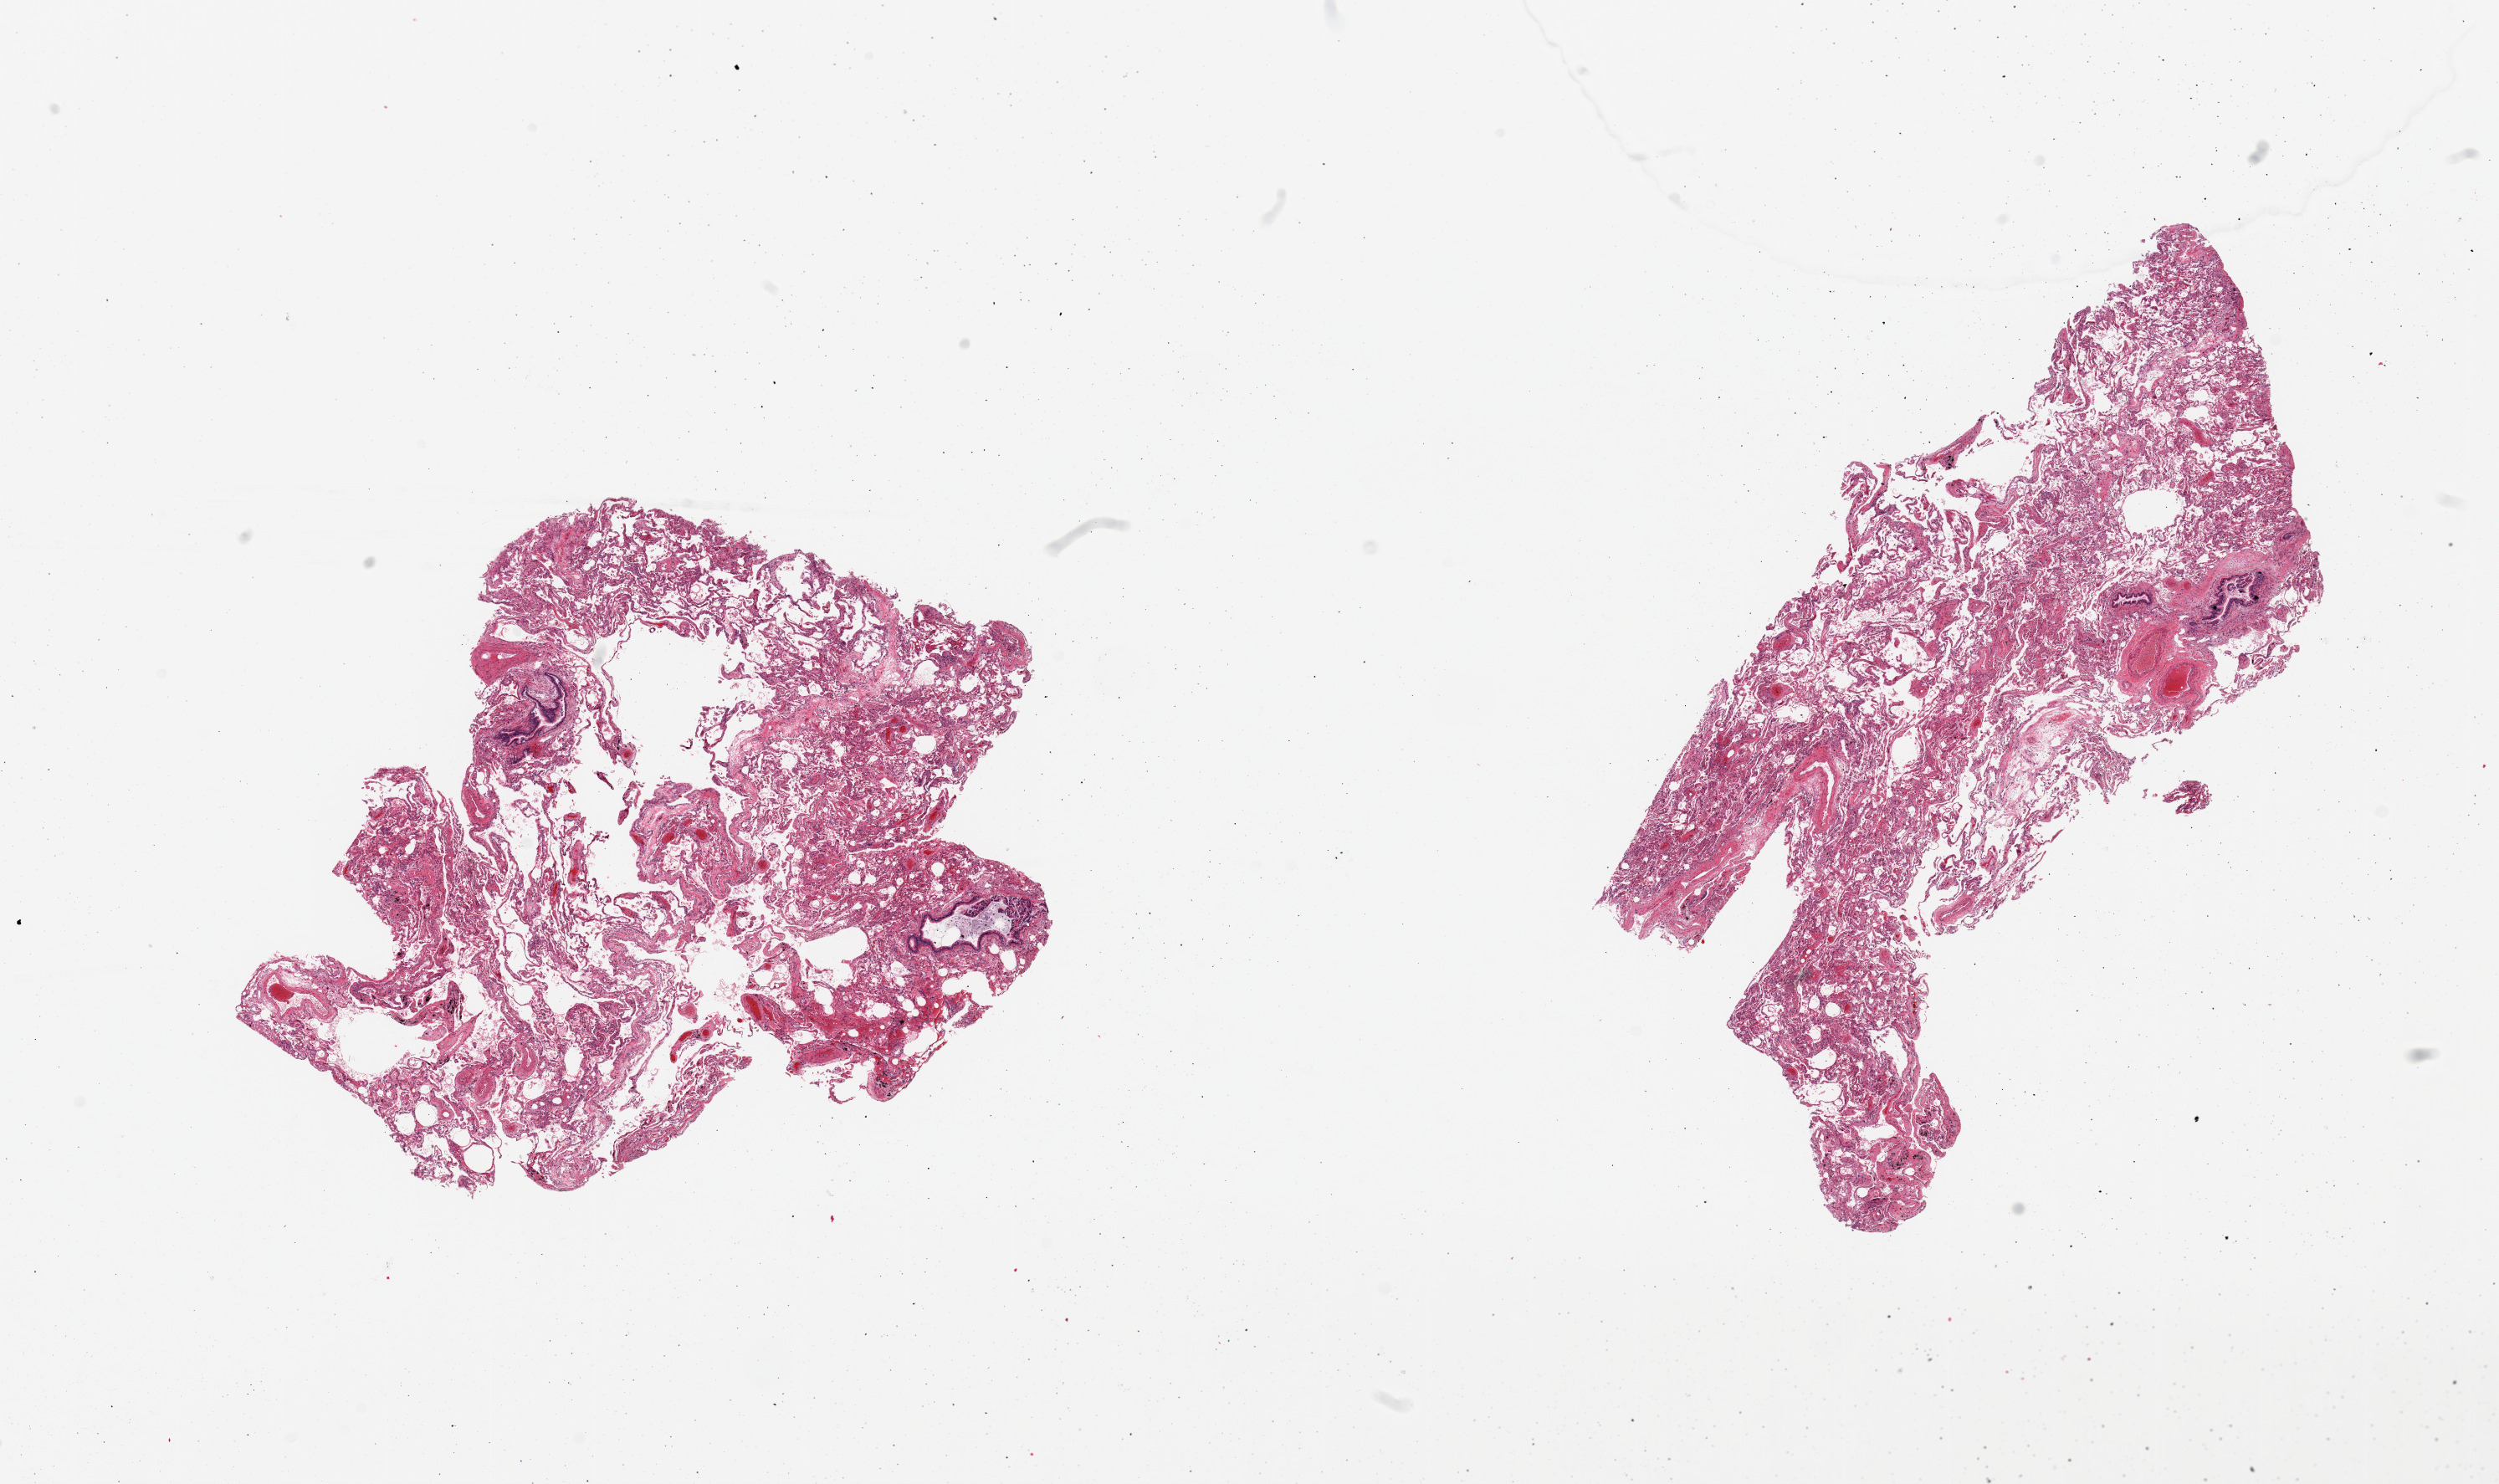
Digitized hematoxylin and eosin (H&E)-stained section, brightfield — whole scanned area (about 23.6 x 14.0 mm) shown as a low-resolution overview. PAXgene-fixed, paraffin-embedded tissue. Sampled site (target tissue): lung. Tissue donor sample. Female donor.
Pathologist's review note for this sample: 2 pieces; emphysema.